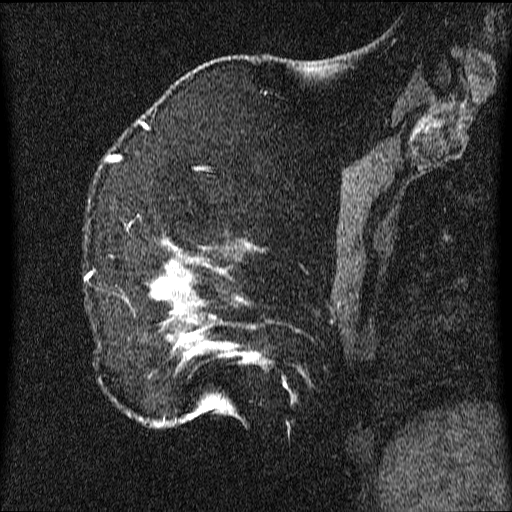
Breast MRI (dynamic contrast-enhanced), one sagittal slice; slice 14 of 64 in the series (ordered by position); dynamic contrast-enhanced series, image 2 of 3 at this slice position (ordered by acquisition); 1.5 T; TE 4.2 ms, TR 9.1 ms; 2.2 mm slice thickness; 512 × 512 image matrix. Patient: female, 52 years.
Annotated regions visible in this slice (semi-automatically segmented with operator editing):
- analysis volume of interest (the breast-tissue region the enhancement analysis was run in; not a lesion): box from (x=86, y=206) to (x=347, y=429) px
- tumour enhancement mask (voxels above the 70 % enhancement threshold inside the analysis volume of interest): (x=152, y=273)–(x=288, y=421)